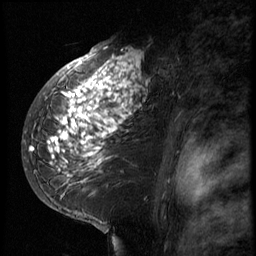
Breast MRI (dynamic contrast-enhanced), one sagittal slice. Slice 43 of 66 in the series (ordered by position). 3 images stored at this slice position (order not interpretable as contrast timing). 1.5 T. TE 4.2 ms, TR 8.9 ms. 256 × 256 image matrix, field of view 200 × 200 mm. Female patient, age 39 years. Case-level facts recorded for this patient, not image findings: setting: breast cancer imaged before/during neoadjuvant chemotherapy; receptor status: HER2-positive.
Outlined on this slice (semi-automatically segmented with operator editing):
- analysis volume of interest (the breast-tissue region the enhancement analysis was run in; not a lesion): bounding box <29,44,166,196> (left, top, right, bottom; pixels)
- tumour enhancement mask (voxels above the 140 % enhancement threshold inside the analysis volume of interest): <29,46,149,182>